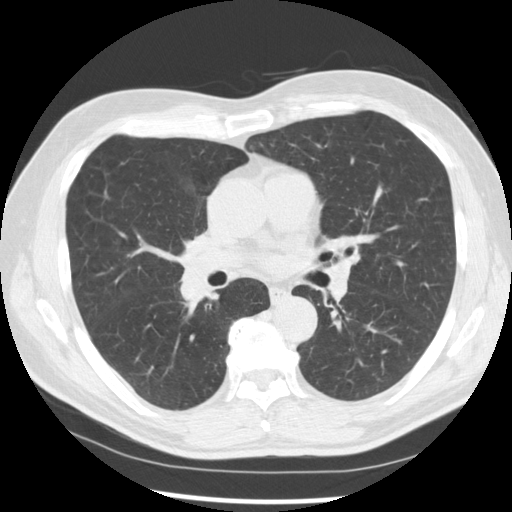
Low-dose screening chest CT, one axial slice; reconstruction kernel STANDARD; lung window (W 1500 / L -600 HU); 2.5 mm slice thickness; 512 × 512 image matrix.
Structures marked on this image (outlined manually by an expert reader):
- lesion 1 (tumor, middle lobe of right lung): box from (x=179, y=269) to (x=210, y=305) px